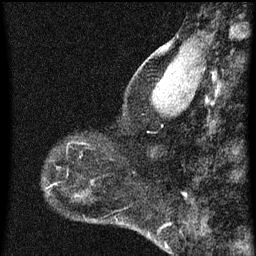
Breast MRI (dynamic contrast-enhanced), one sagittal slice. Position 19 of 60 along the scan axis. Dynamic contrast-enhanced series, image 2 of 3 at this slice position (ordered by acquisition). 1.5 T. TE 4.2 ms, TR 8 ms. 2 mm slice thickness. 256 × 256 image matrix, field of view 180 × 180 mm. Patient: female, 44 years.
Structures marked on this image (semi-automatically segmented with operator editing):
- analysis volume of interest (the breast-tissue region the enhancement analysis was run in; not a lesion): bounding box <49,140,95,169> (left, top, right, bottom; pixels)
- tumour enhancement mask (voxels above the 70 % enhancement threshold inside the analysis volume of interest): <69,142,89,157>